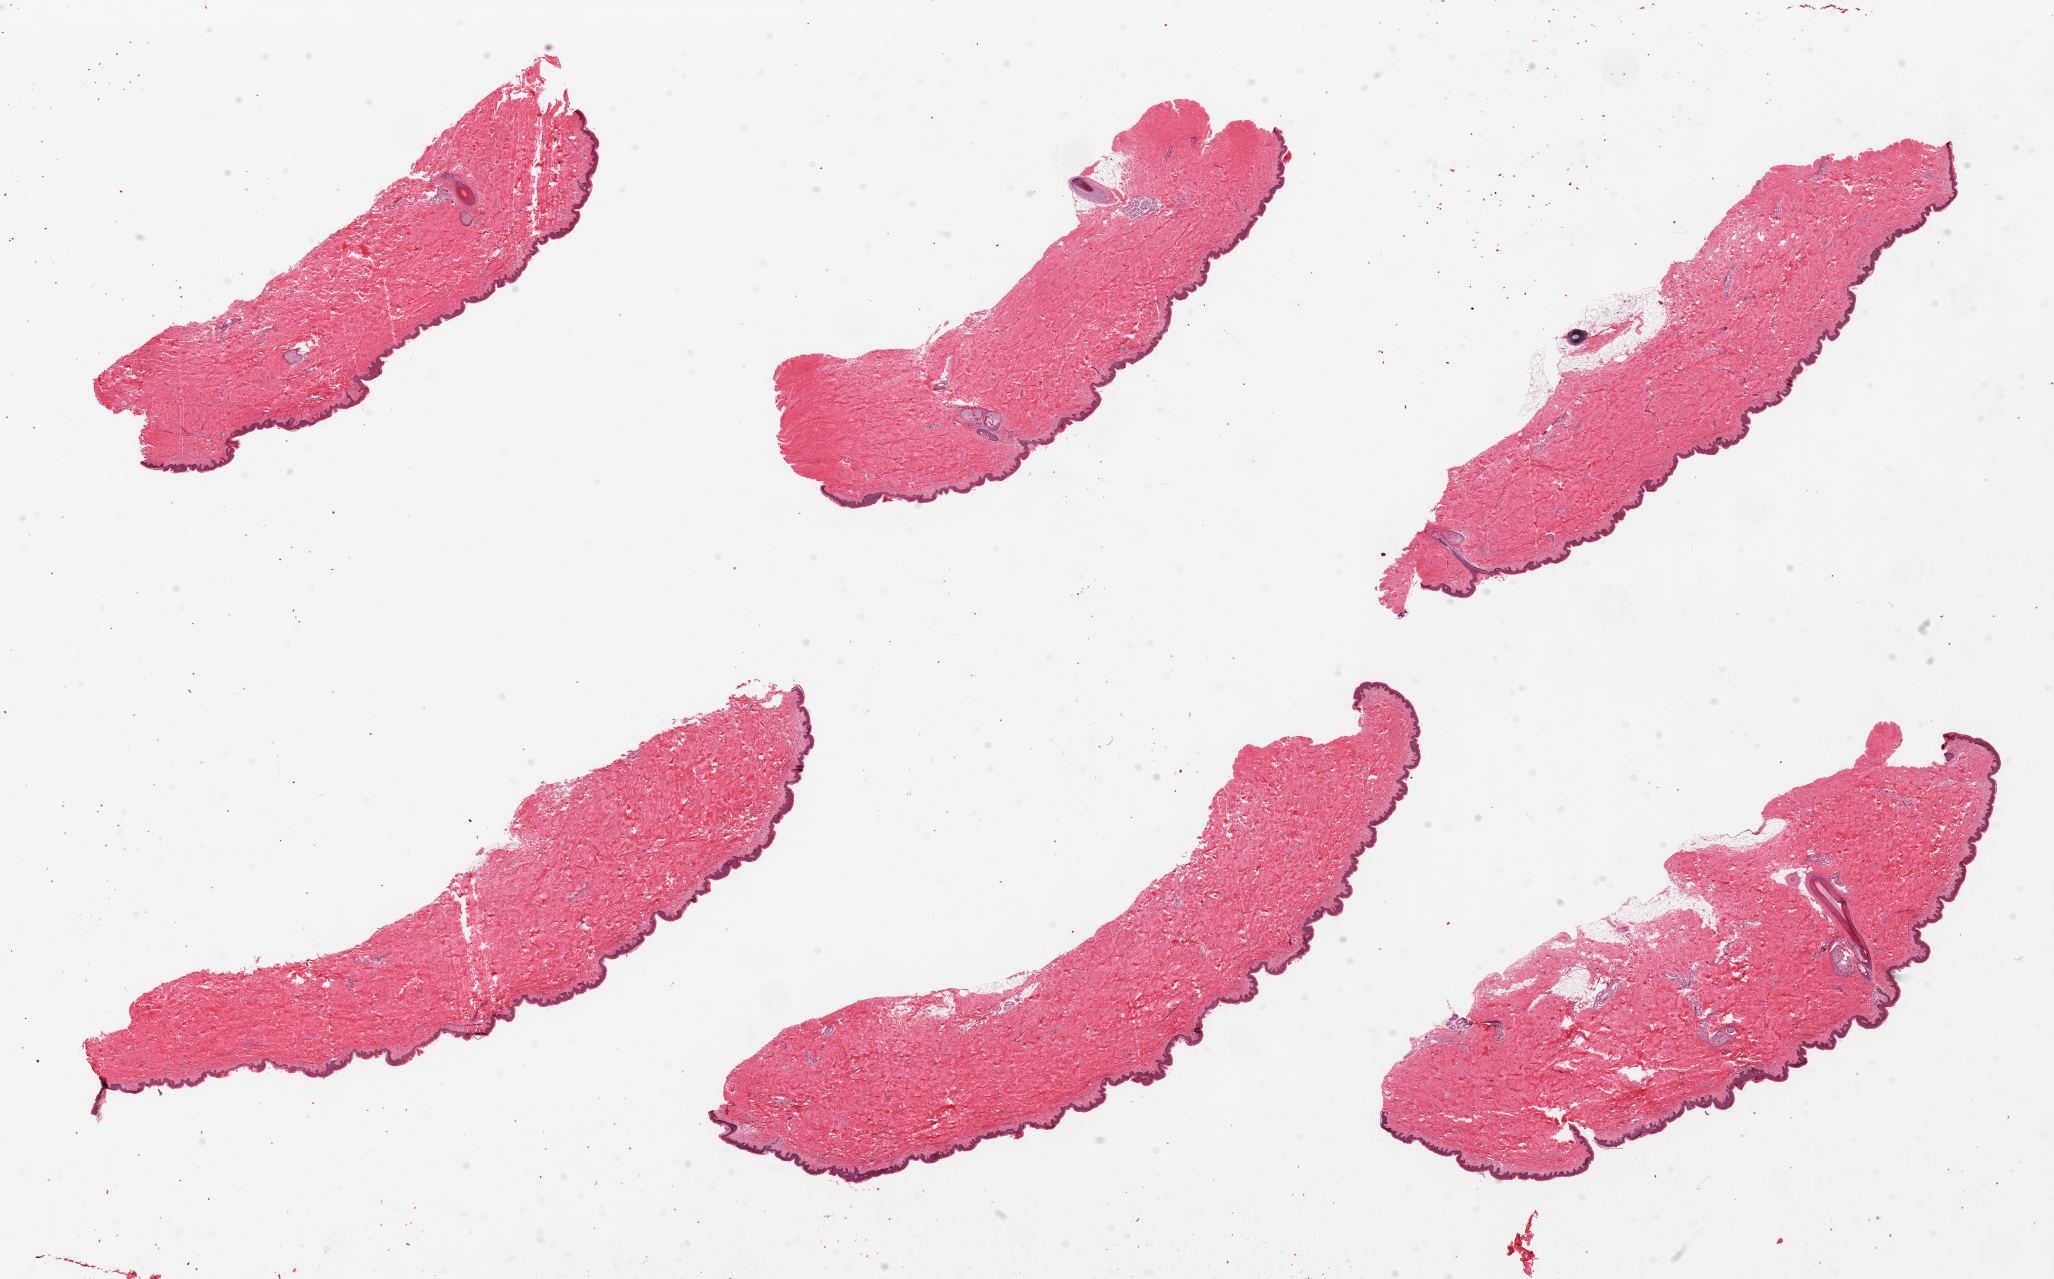
H&E whole-slide image, low-resolution overview of the scanned area, about 32.5 x 20.2 mm (acquisition: 20x scan). PAXgene-fixed paraffin-embedded (PFPE) section. Sampled site (target tissue): skin of suprapubic region. Donor tissue sample. Donor sex: male.
* reviewer comment on this tissue sample: 6 pieces, predominantly well trimmed, few pieces with minimal attached adipose tissue